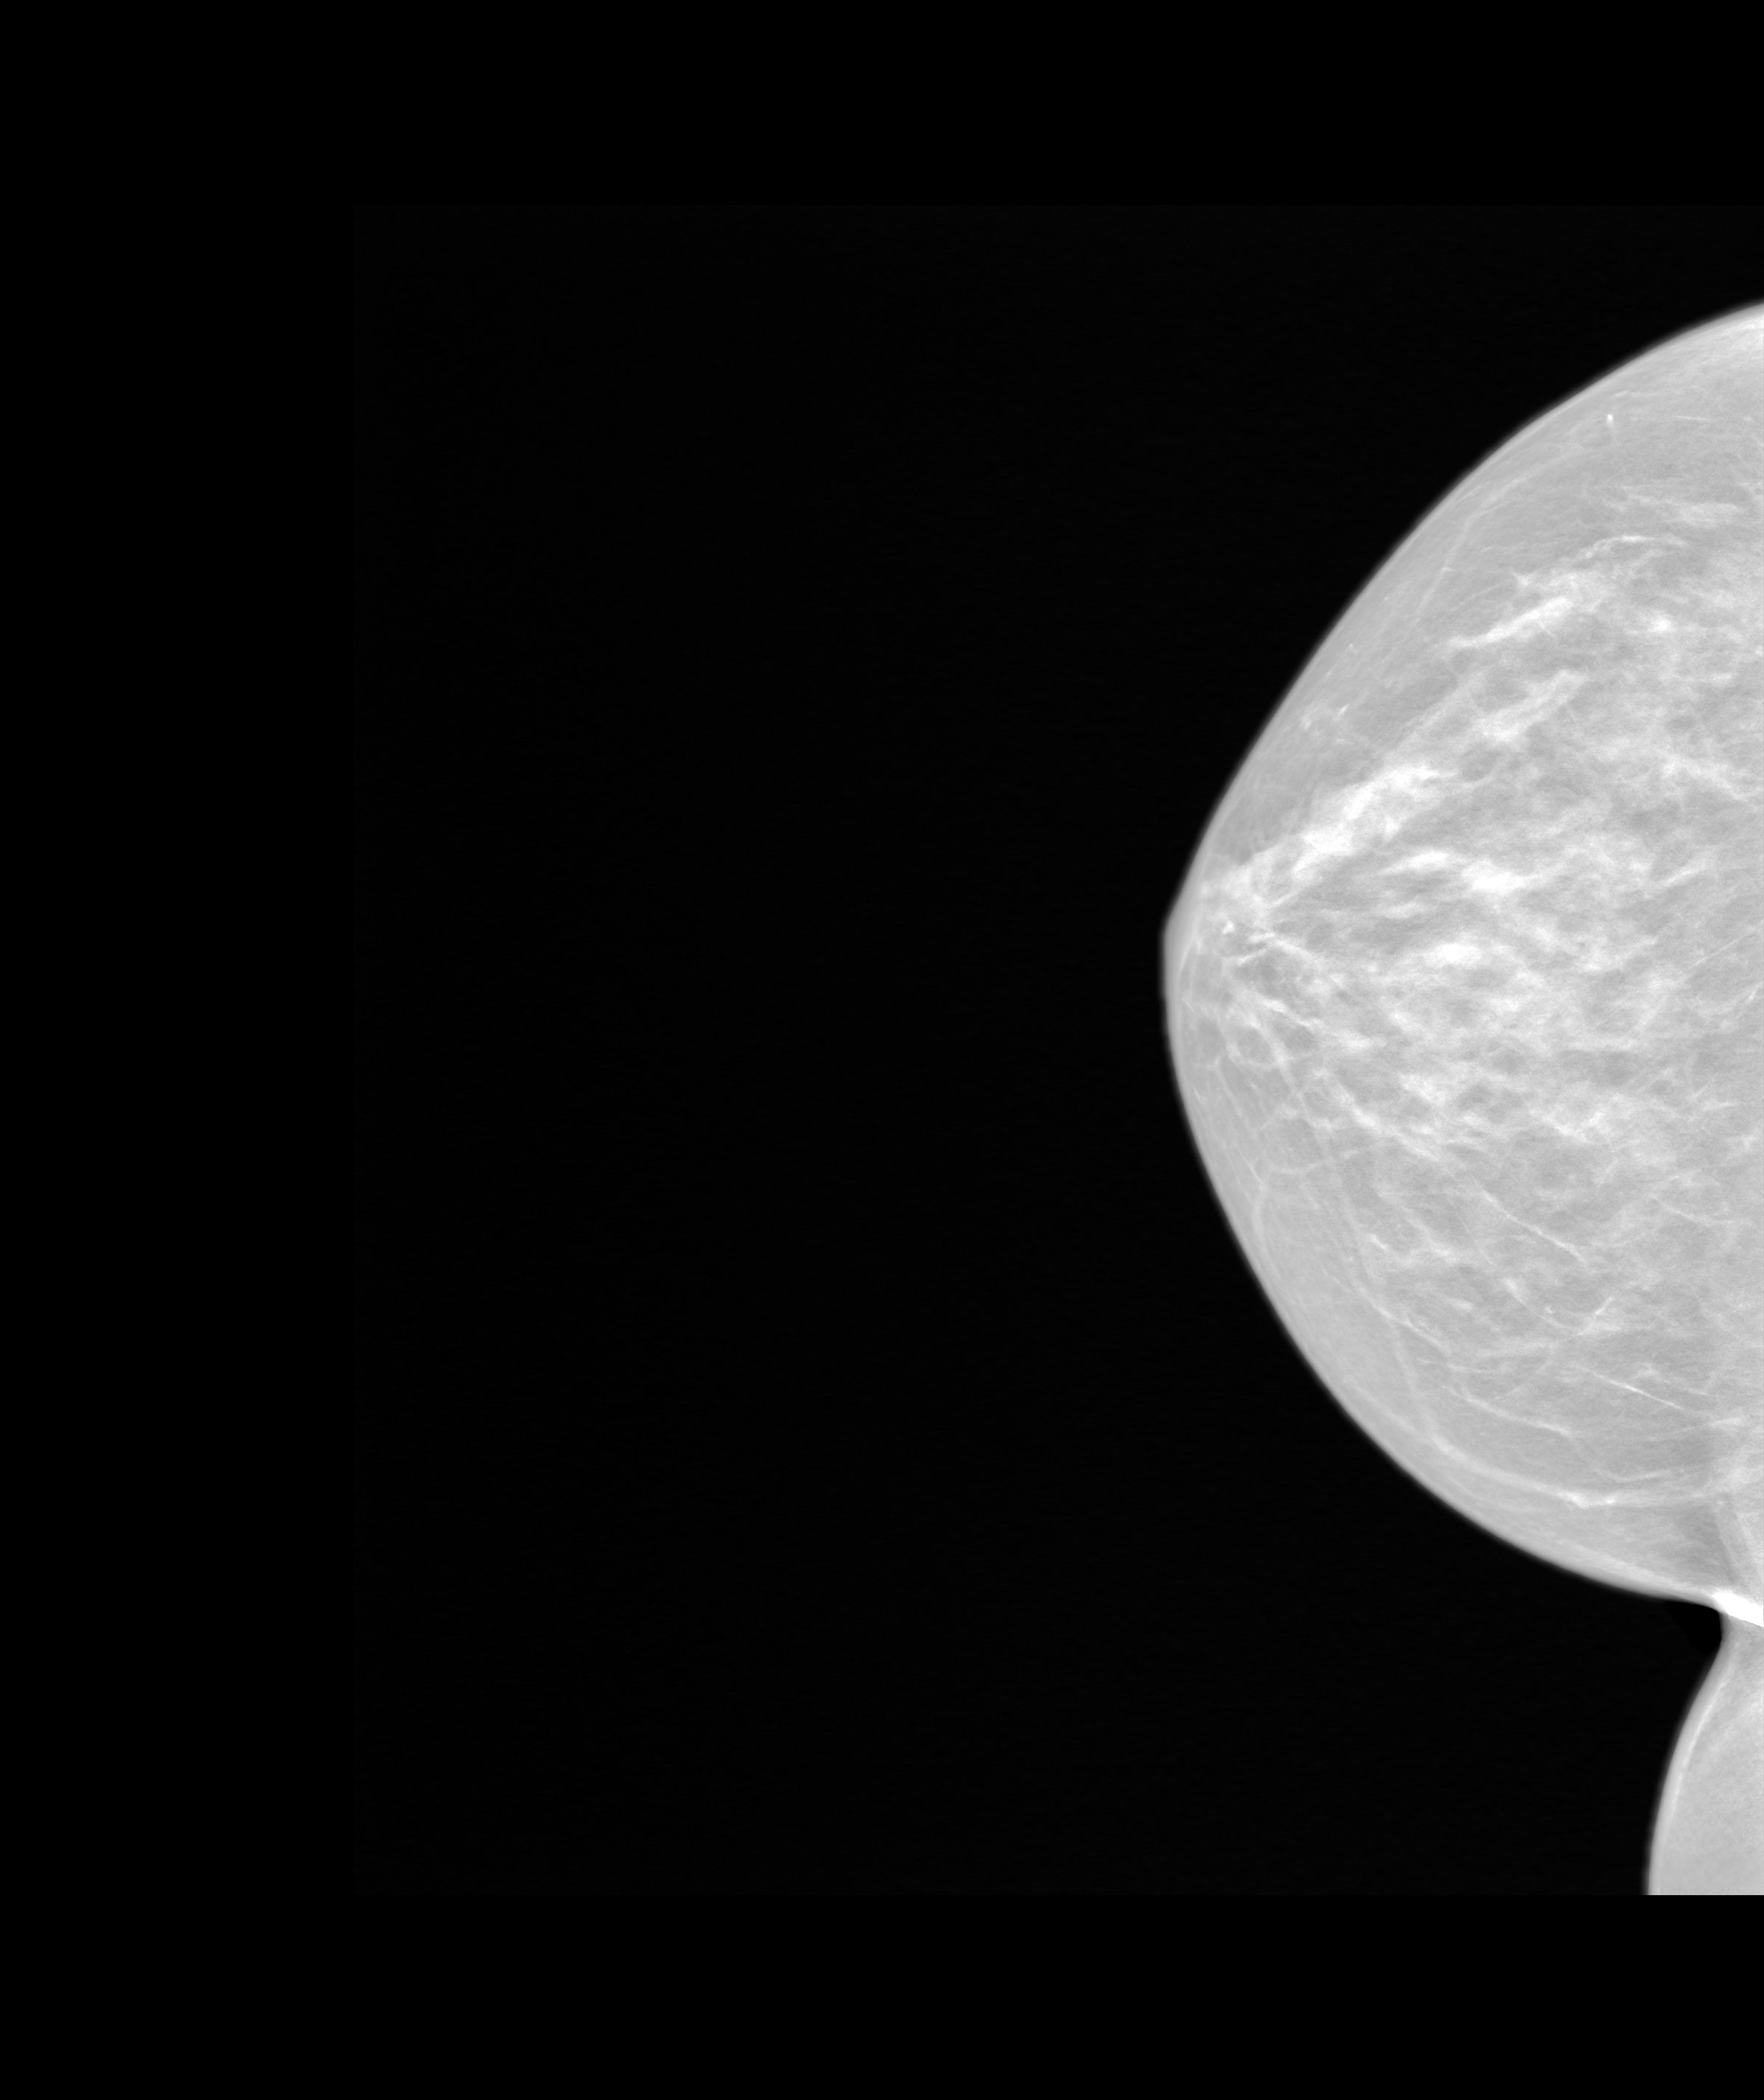
Screening examination. Patient aged 59 years (female).
Image type: synthesized 2-D view from tomosynthesis. Breast: right. Projection: craniocaudal (CC) view.